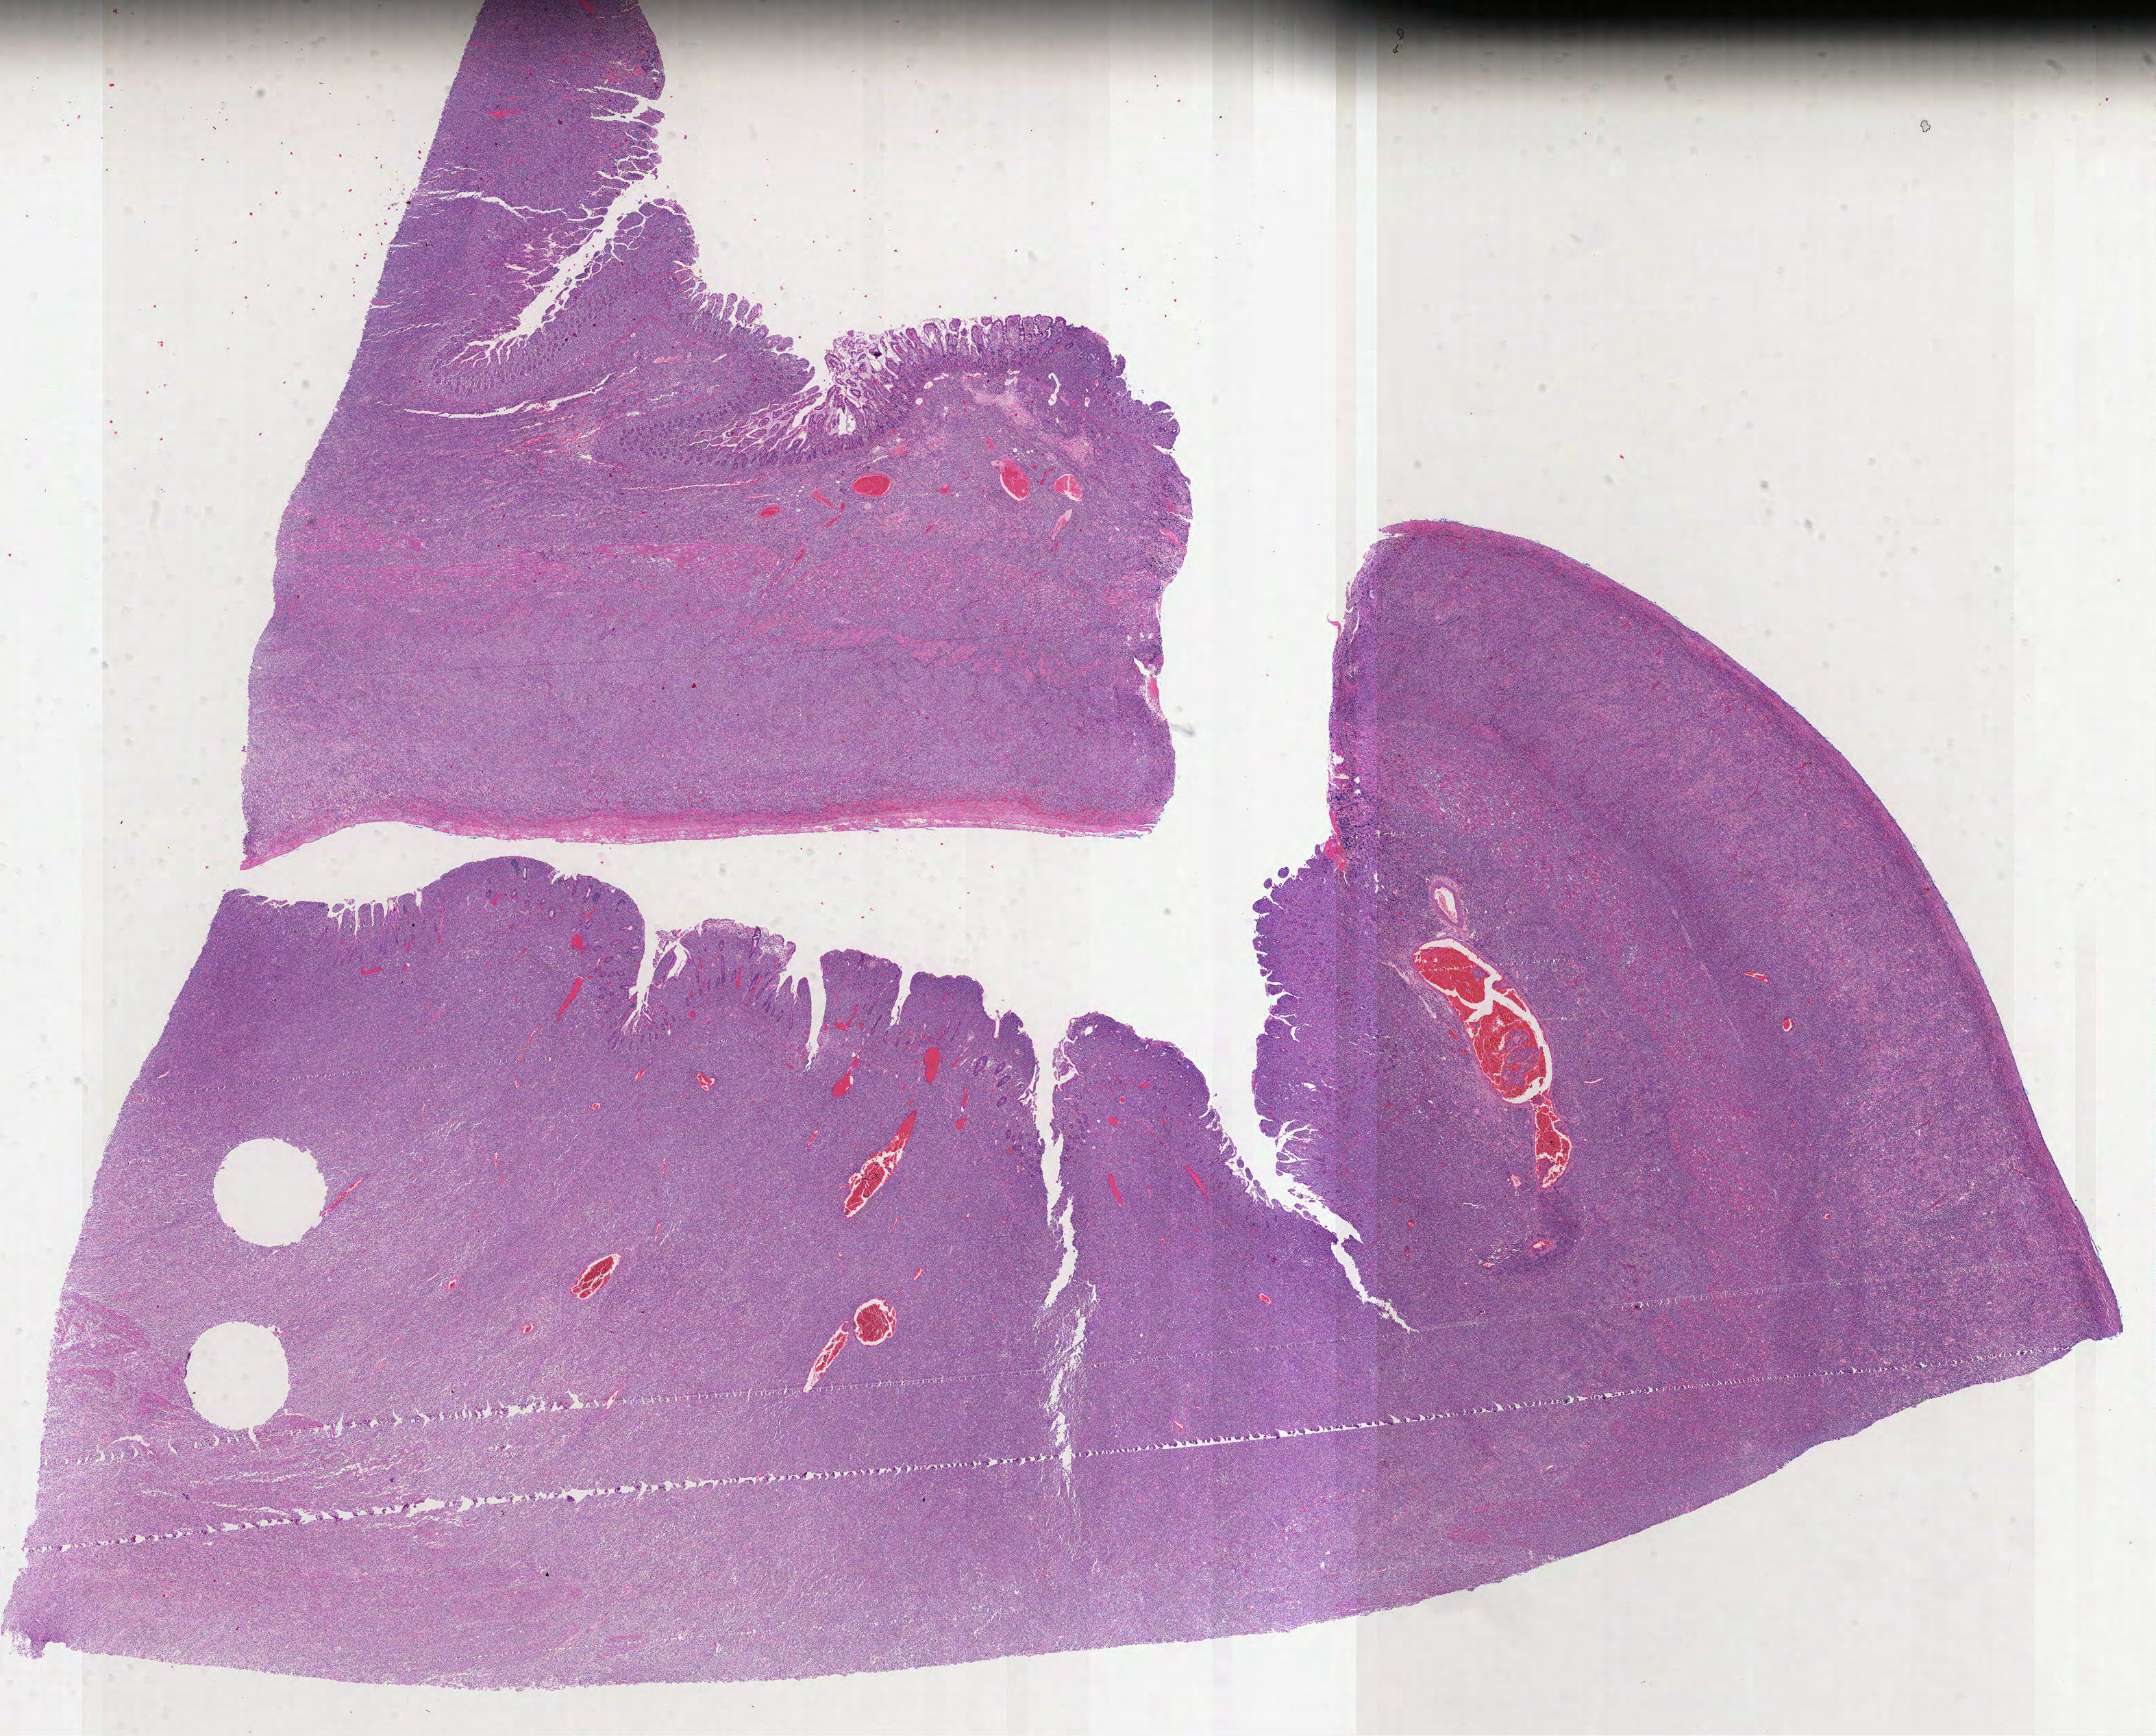
Digitized H&E tissue section (whole slide) — whole scanned area (about 25.4 x 20.4 mm, slide scanned at 40x) shown as a low-resolution overview, FFPE section, lymphoid tissue, primary tumour sample. Male patient; age at initial diagnosis 42 years.
- histologic diagnosis: Diffuse large B-cell lymphoma, NOS (small intestine, NOS)